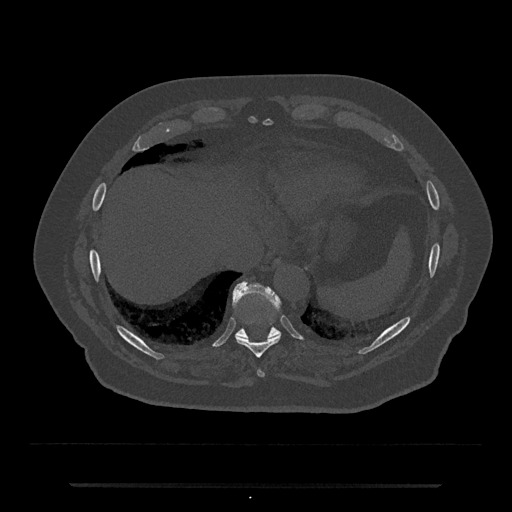
CT including the spine, one axial slice. Slice 740 of 797 in the series (ordered by position). Bone window (W 1800 / L 400 HU). 512 × 512 image matrix, field of view 434 × 434 mm. Patient: male, 80 years. Case-level facts recorded for this patient, not image findings: primary cancer: prostate.
Outlined on this slice (semi-automatic segmentation, software-assisted and operator-edited):
- T10 vertebra: bounding box (x1, y1, x2, y2) in pixels: (233, 282, 281, 338)
- T8 vertebra: (258, 370, 264, 377)
- T9 vertebra: (236, 321, 281, 358)